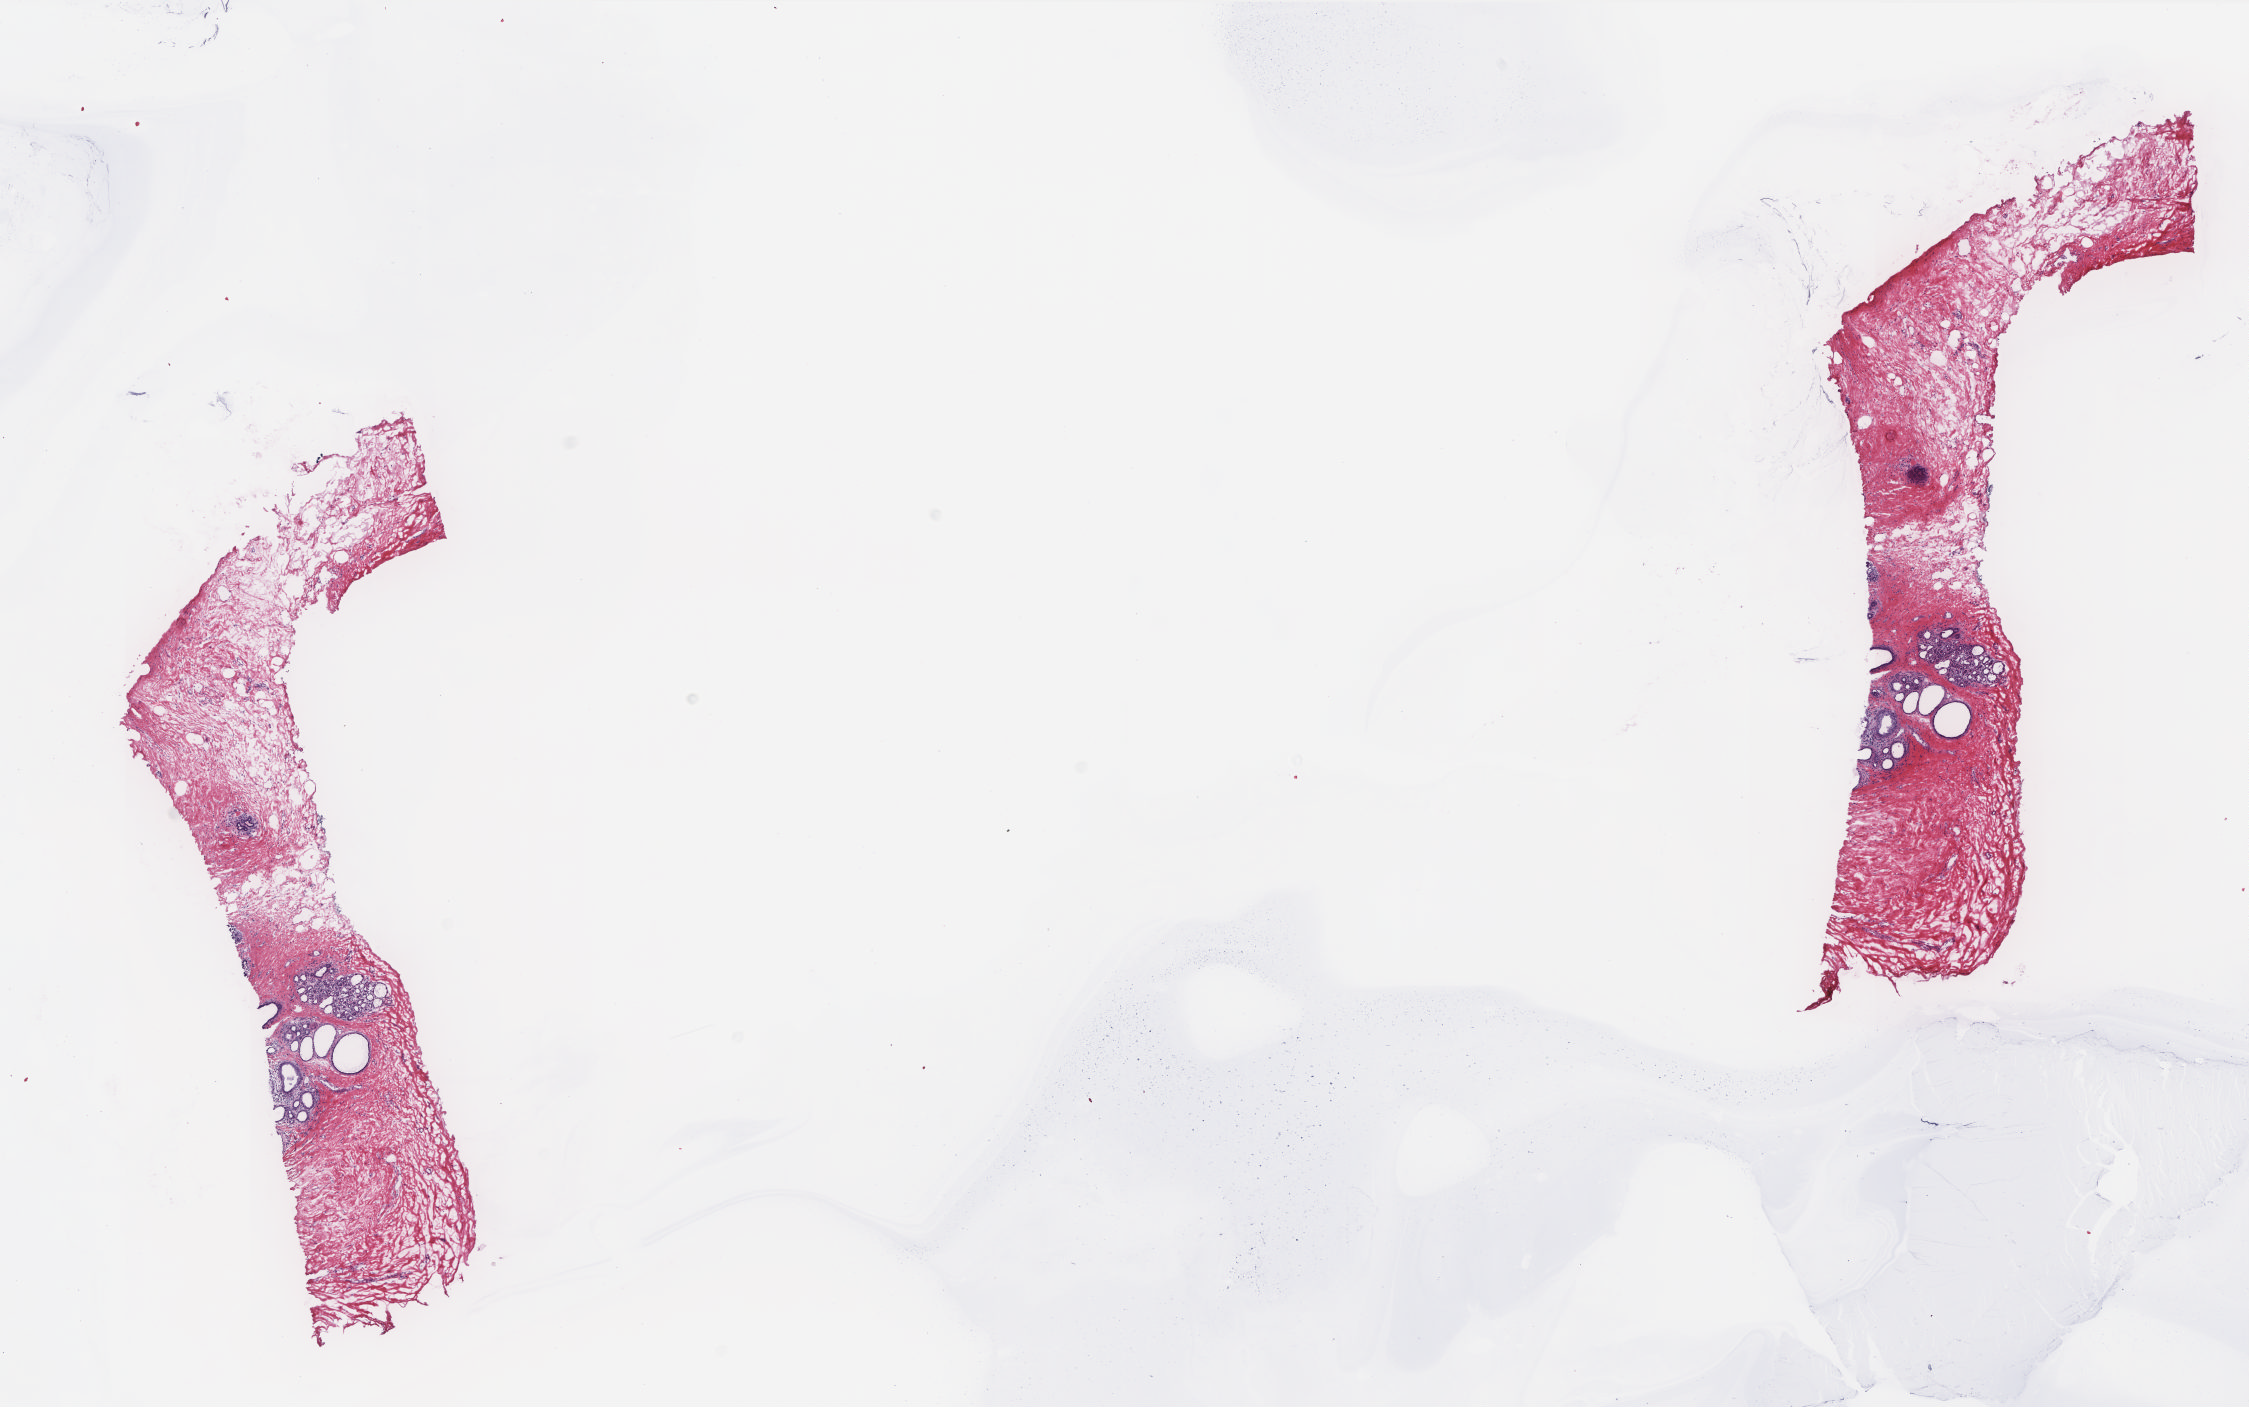
Digitized H&E tissue section (whole slide), low-resolution overview of the scanned area, about 18.0 x 11.2 mm (acquisition: 20x scan). Frozen section. Breast, solid tissue normal (non-tumour tissue) sample. Female, age 40 years at initial diagnosis. Composition of this section per pathologist review: tumour cells 0%, tumour nuclei 0%, normal cells 20%, stromal cells 80%, necrosis 0%. Inflammatory infiltration, as recorded: lymphocyte infiltration 1%, monocyte infiltration 0%, neutrophil infiltration 0%.
This section: solid tissue normal (non-tumour) sample from the same patient. Patient diagnosis: Lobular carcinoma, NOS.